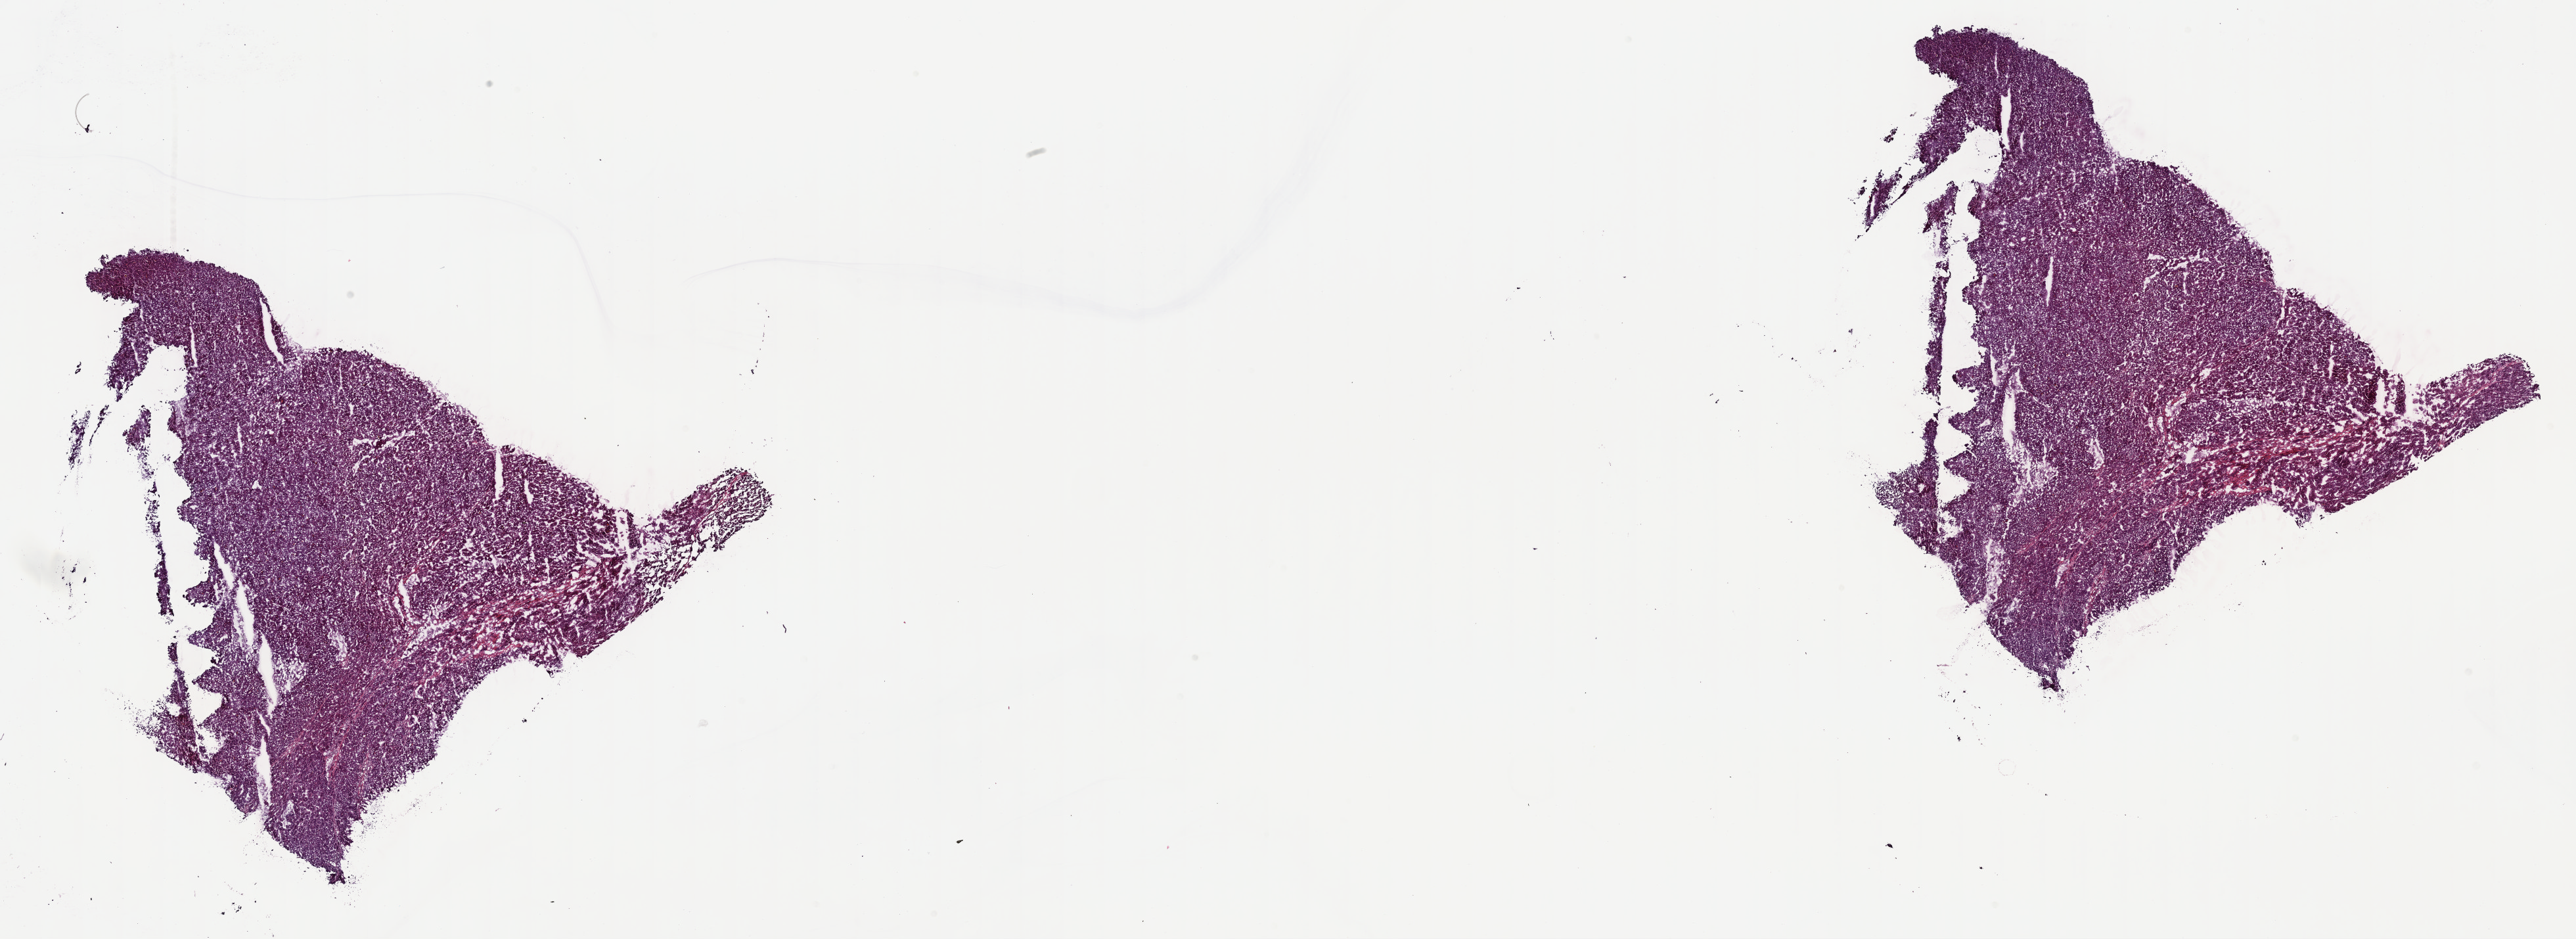
H&E-stained whole-slide image, whole scanned area (about 31.7 x 11.6 mm, slide scanned at 40x) shown as a low-resolution overview, frozen section, liver, primary tumour sample. Patient: male, age at initial diagnosis 48 years. Histologic grade: G4 (undifferentiated). Slide review estimates, as recorded: tumour cells 83%, tumour nuclei 90%, normal cells 0%, stromal cells 15%, necrosis 2%. Infiltration values recorded for this section: lymphocyte infiltration 6%, monocyte infiltration 1%, neutrophil infiltration 0%.
AJCC pathologic stage: I (6th edition). Pathologic diagnosis: Hepatocellular carcinoma, NOS.